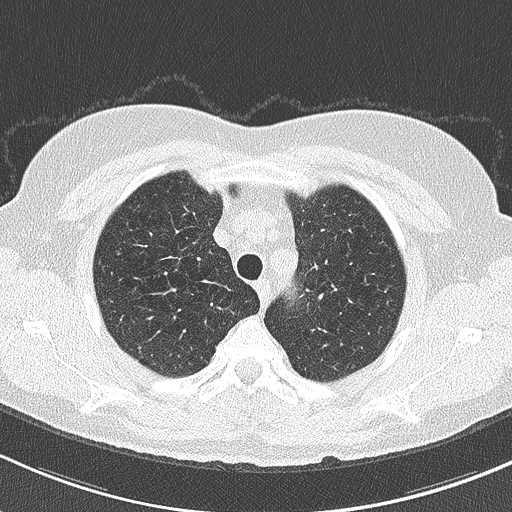
Chest CT (low-dose screening protocol), one axial image; first (baseline) screen; lung window (W 1500 / L -600 HU); slice 35 of 202 in the series. Female participant, aged 60 years at enrolment. Former smoker at enrolment.
- Expert reader's lesion annotation, bounding box <105,240,133,268> (left, top, right, bottom; pixels).
- Reader record for this screening exam (exam-level; its link to the box is not recorded): non-calcified nodule or mass ≥4 mm, right upper lobe, 4 × 4 mm, smooth margins, soft tissue attenuation.
- Later outcome: lung cancer diagnosed 216 days after this screen — acinar cell carcinoma, right upper lobe, well differentiated (G1), stage IA (AJCC 6th edition), 7 mm at pathology.